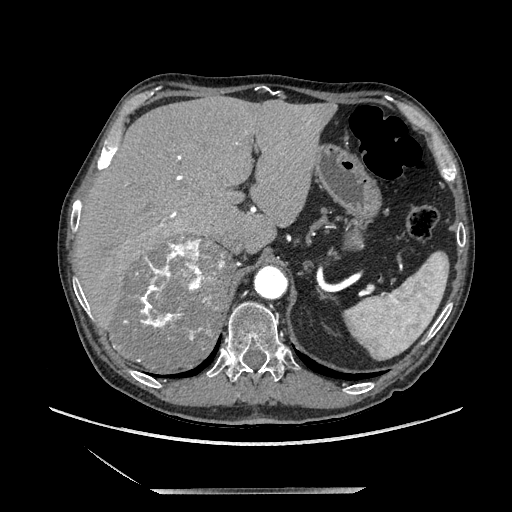
Contrast-enhanced abdominal CT, one axial slice; slice 154 of 243 in the series (ordered by position); soft-tissue window (W 400 / L 40 HU); 1.25 mm slice thickness; 512 × 512 image matrix, field of view 420 × 420 mm. Male patient. From the clinical record (not read from this slice): diagnosis: adrenocortical carcinoma; tumour side: right adrenal; tumour size at pathology: 16 cm; Ki-67 index: 17 %; stage (as recorded): 3.
Outlined on this slice (semi-automatic segmentation, software-assisted and operator-edited):
- mass: box from (x=113, y=237) to (x=233, y=372) px